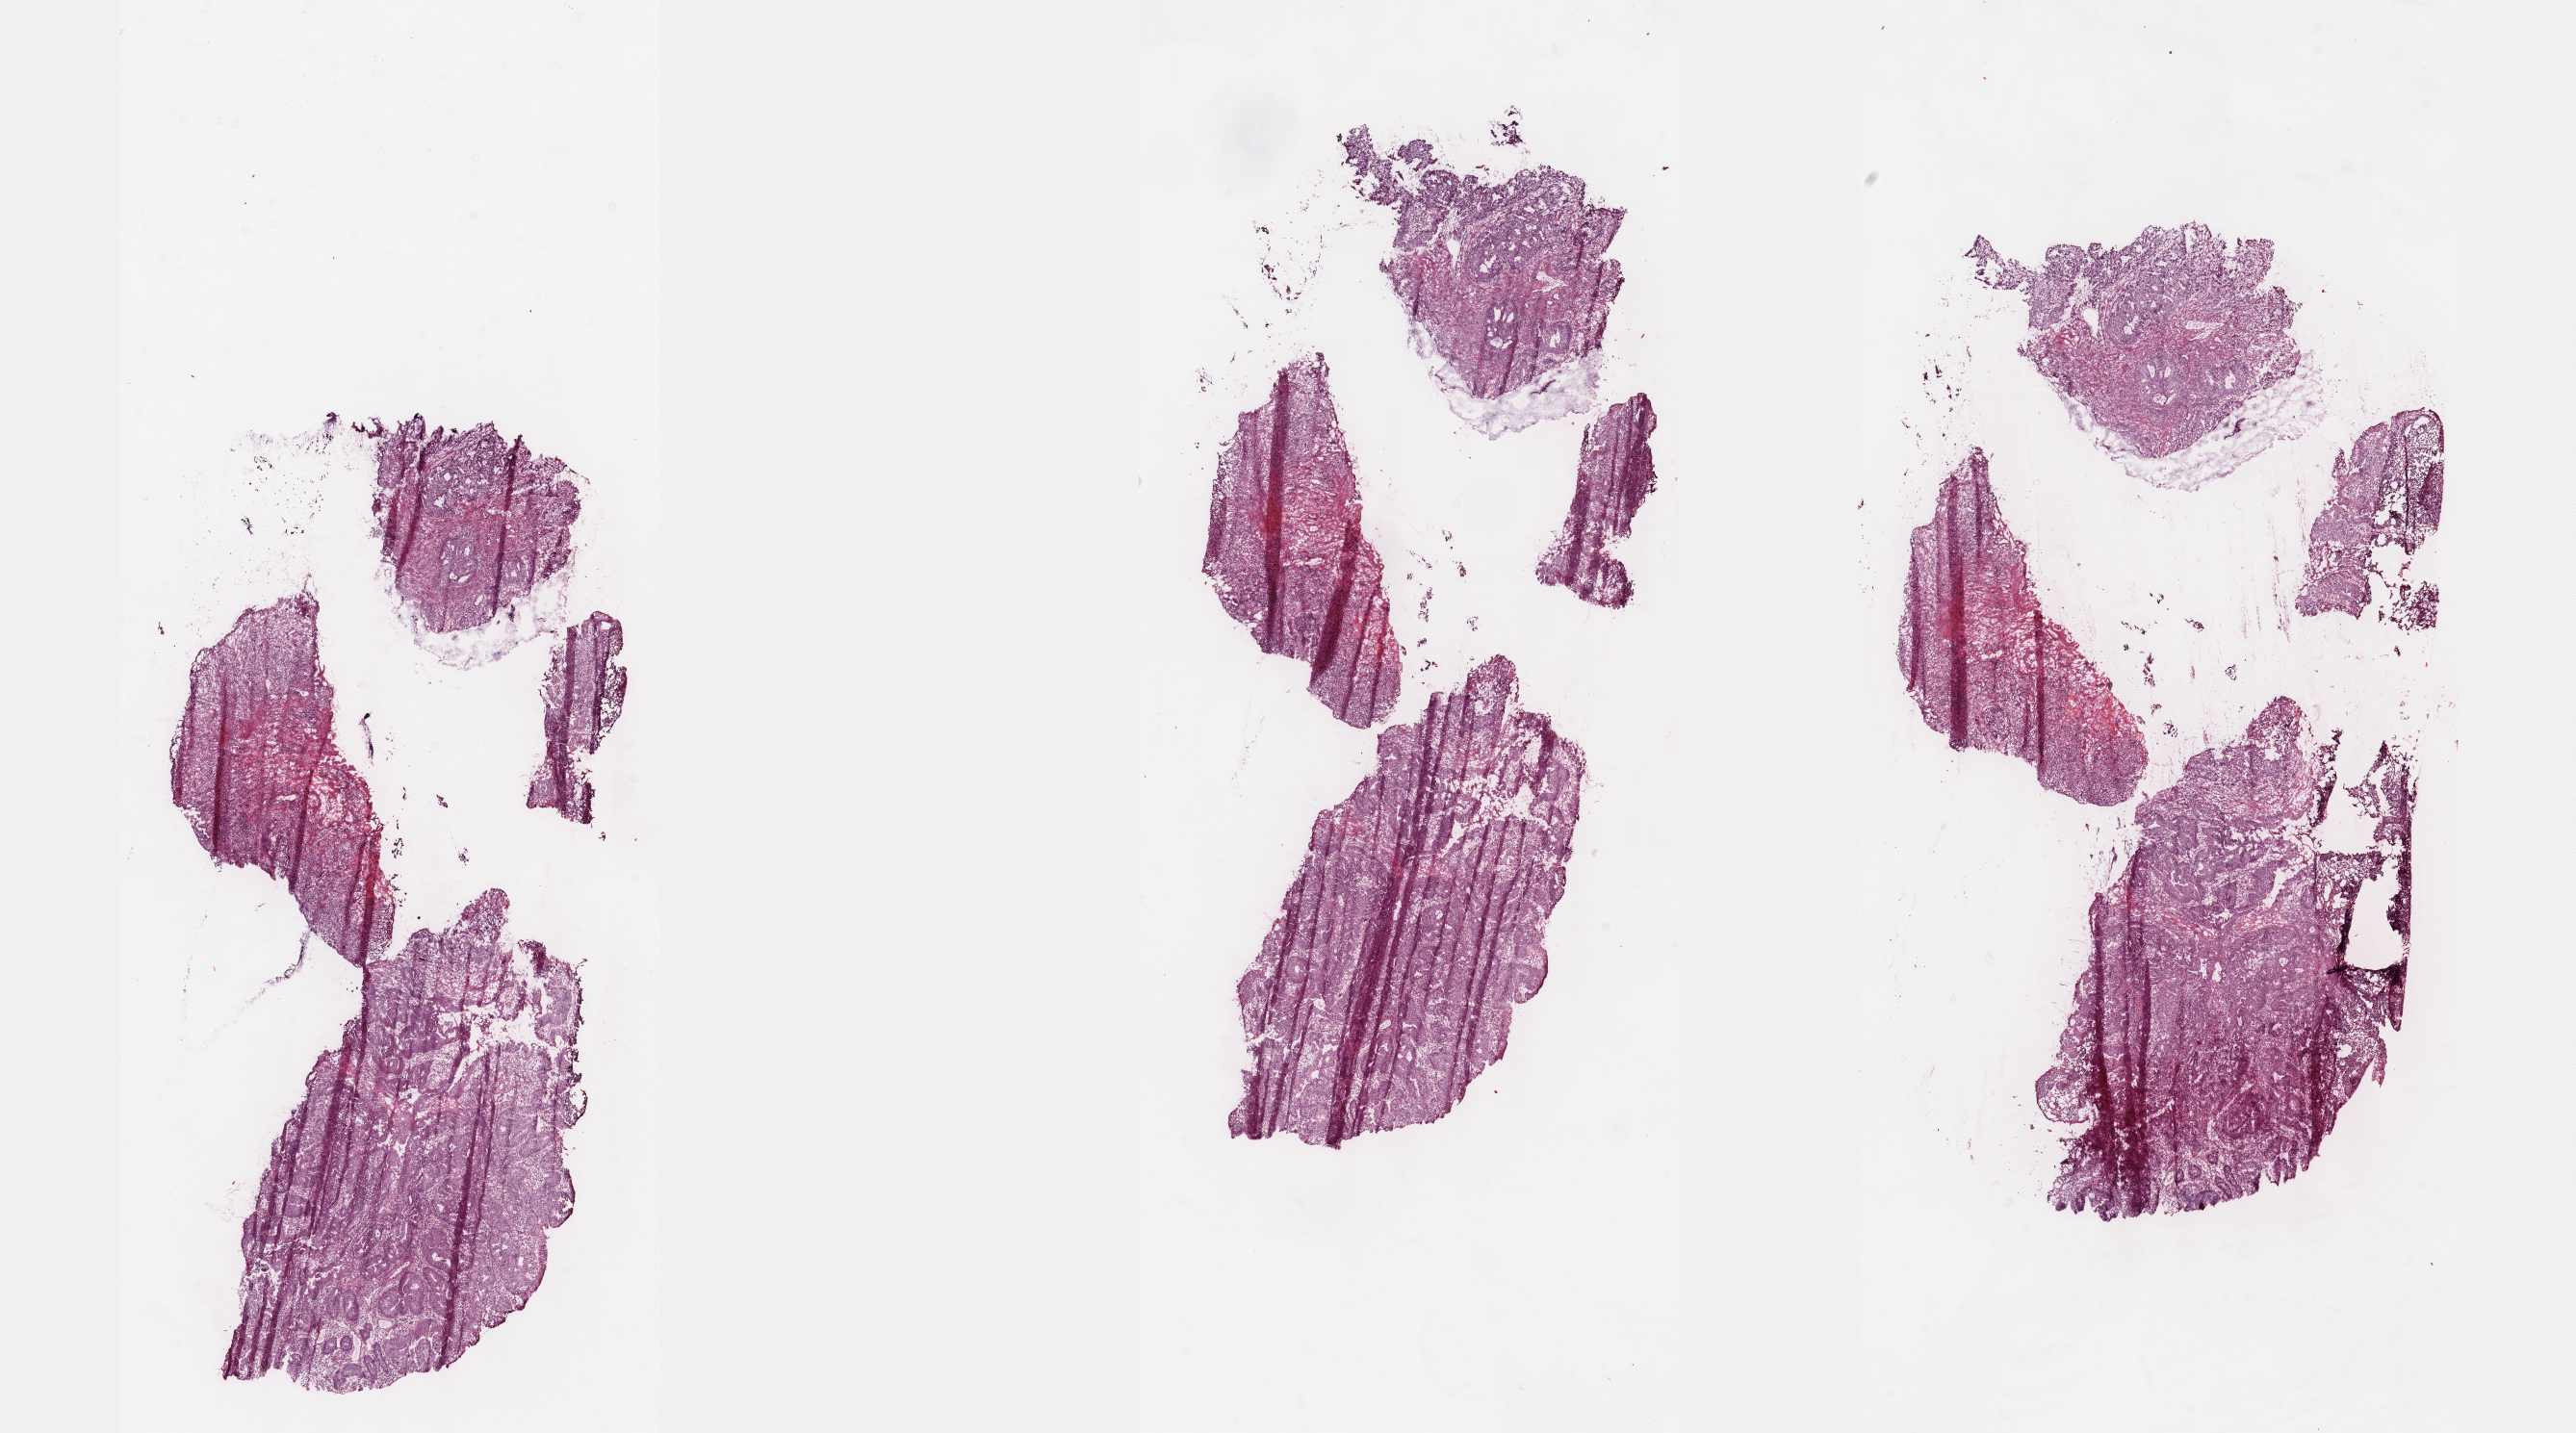
Whole-slide histology image, Hematoxylin and eosin (H&E) stained — whole scanned area (about 21.6 x 12.0 mm) shown as a low-resolution overview; frozen section; primary tumour sample from the rectum. Female patient; age at initial diagnosis 62 years. Pathologist review of this section (percent, as recorded): tumour cells 60%, tumour nuclei 60%, normal cells 0%, stromal cells 39%, necrosis 1%. Inflammatory infiltration, as recorded: lymphocyte infiltration 20%, monocyte infiltration 2%, neutrophil infiltration 1%.
Lymph nodes positive (case pathology): 0 of 11 examined. Histologic diagnosis: Adenocarcinoma, NOS. AJCC pathologic stage: I.